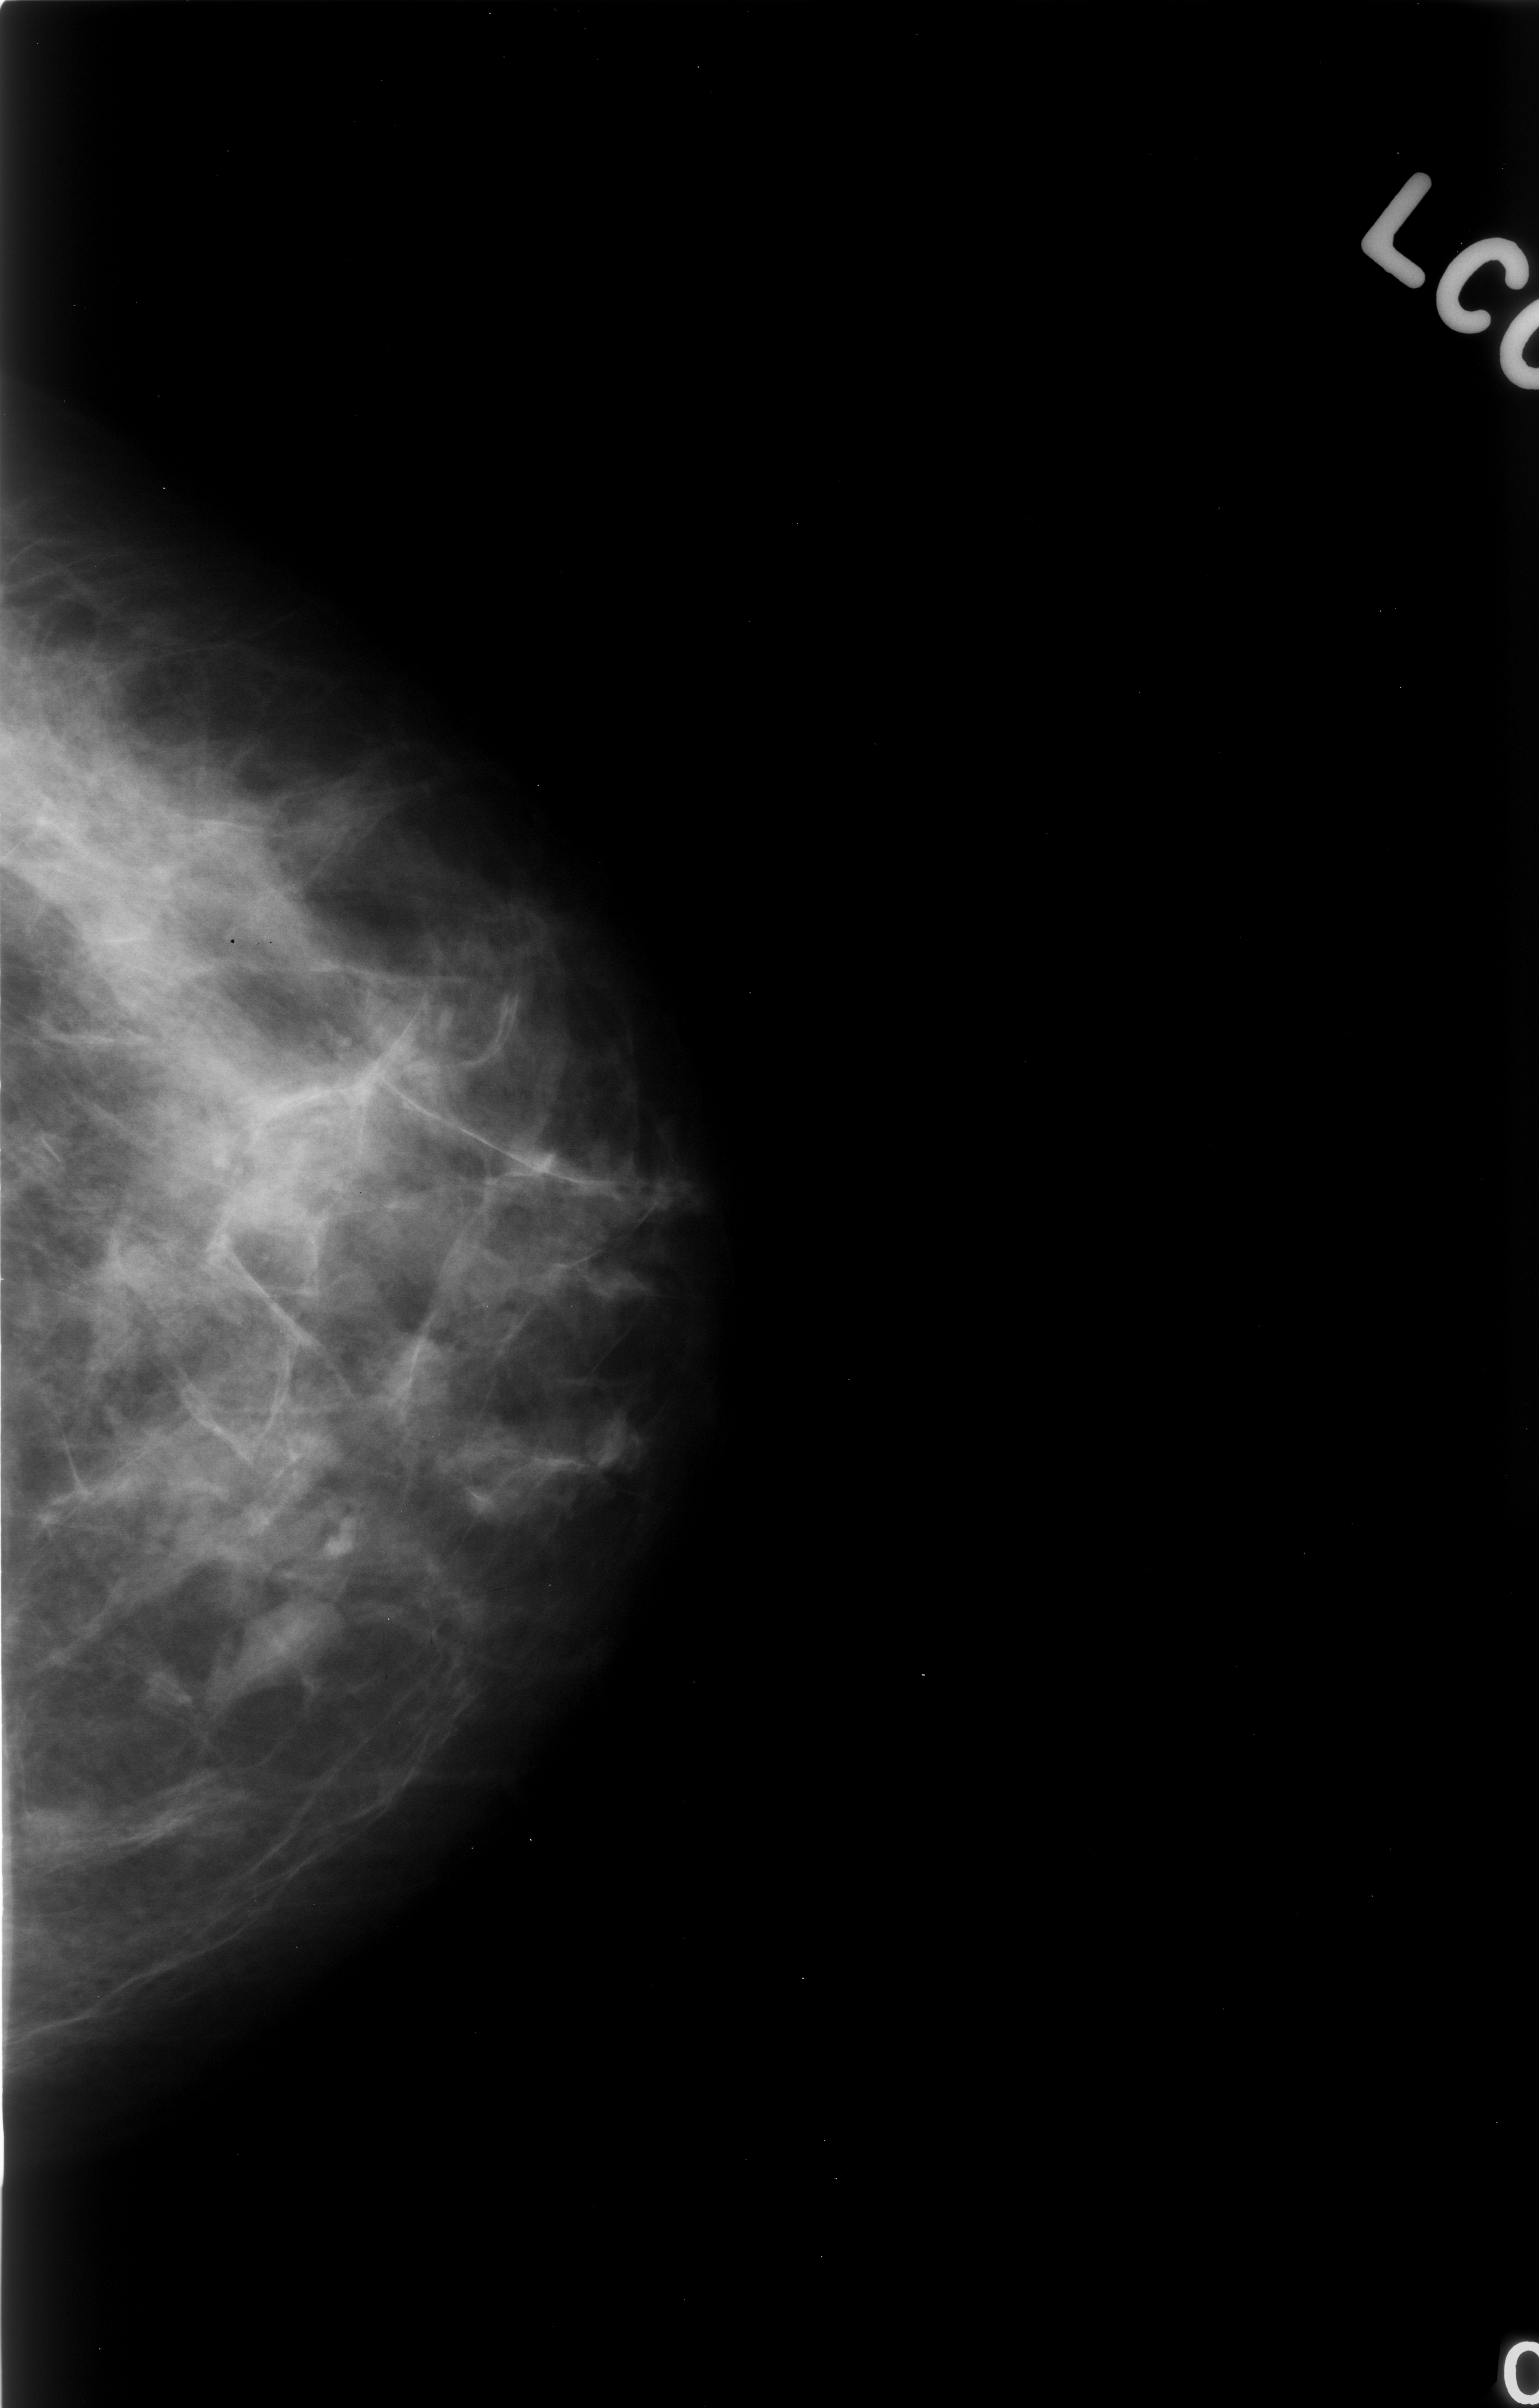
Mammogram (digitized film); left breast; craniocaudal (CC) view.
Abnormality record for this image: mass, shape lobulated, margins circumscribed; BI-RADS assessment category 3; subtlety rating 5 on a 1 (subtle) to 5 (obvious) scale; pathology (as recorded): benign.